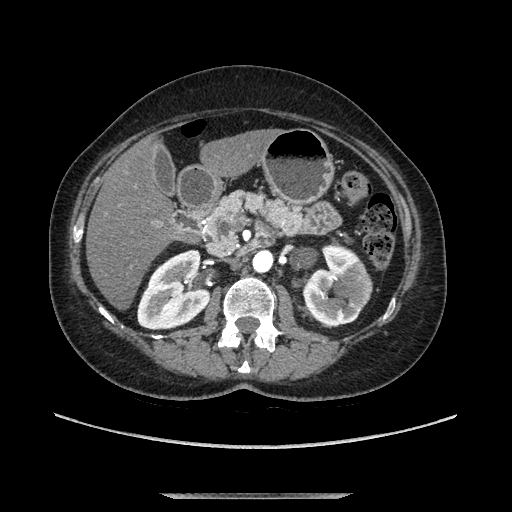
Contrast-enhanced abdominal CT, one axial slice. Position 53 of 169 along the scan axis. Soft-tissue window (W 400 / L 40 HU). 1.25 mm slice thickness. 512 × 512 image matrix, field of view 400 × 400 mm. Female patient. From the clinical record (not read from this slice): diagnosis: adrenocortical carcinoma; tumour side: left adrenal; tumour size at pathology: 9 cm; Ki-67 index: 2 %; stage (as recorded): 3.
Structures marked on this image (semi-automatic segmentation, software-assisted and operator-edited):
- mass: bounding box (x1, y1, x2, y2) in pixels: (291, 250, 317, 270)